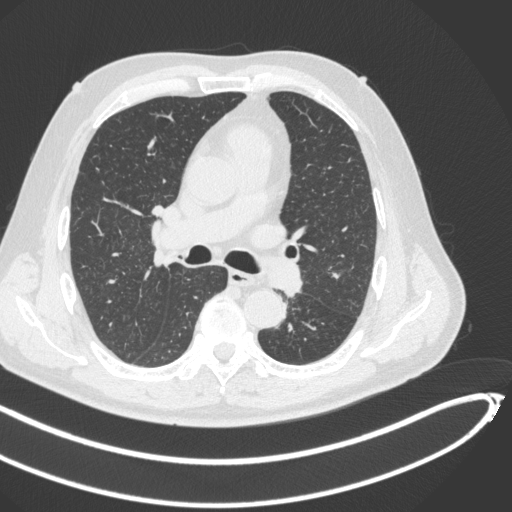
Chest CT, one axial slice; position 277 of 466 along the scan axis; reconstruction kernel B31f; 120 kVp; lung window (W 1500 / L -600 HU); 1 mm slice thickness; 512 × 512 image matrix, field of view 400 × 400 mm. Male patient, age 64 years. Case-level facts recorded for this patient, not image findings: clinical TNM (as recorded): T1c N0 M0.
Structures marked on this image (bounding box drawn by a radiologist):
- lung tumour (recorded histology: squamous cell carcinoma): bounding box <265,253,303,296> (left, top, right, bottom; pixels)